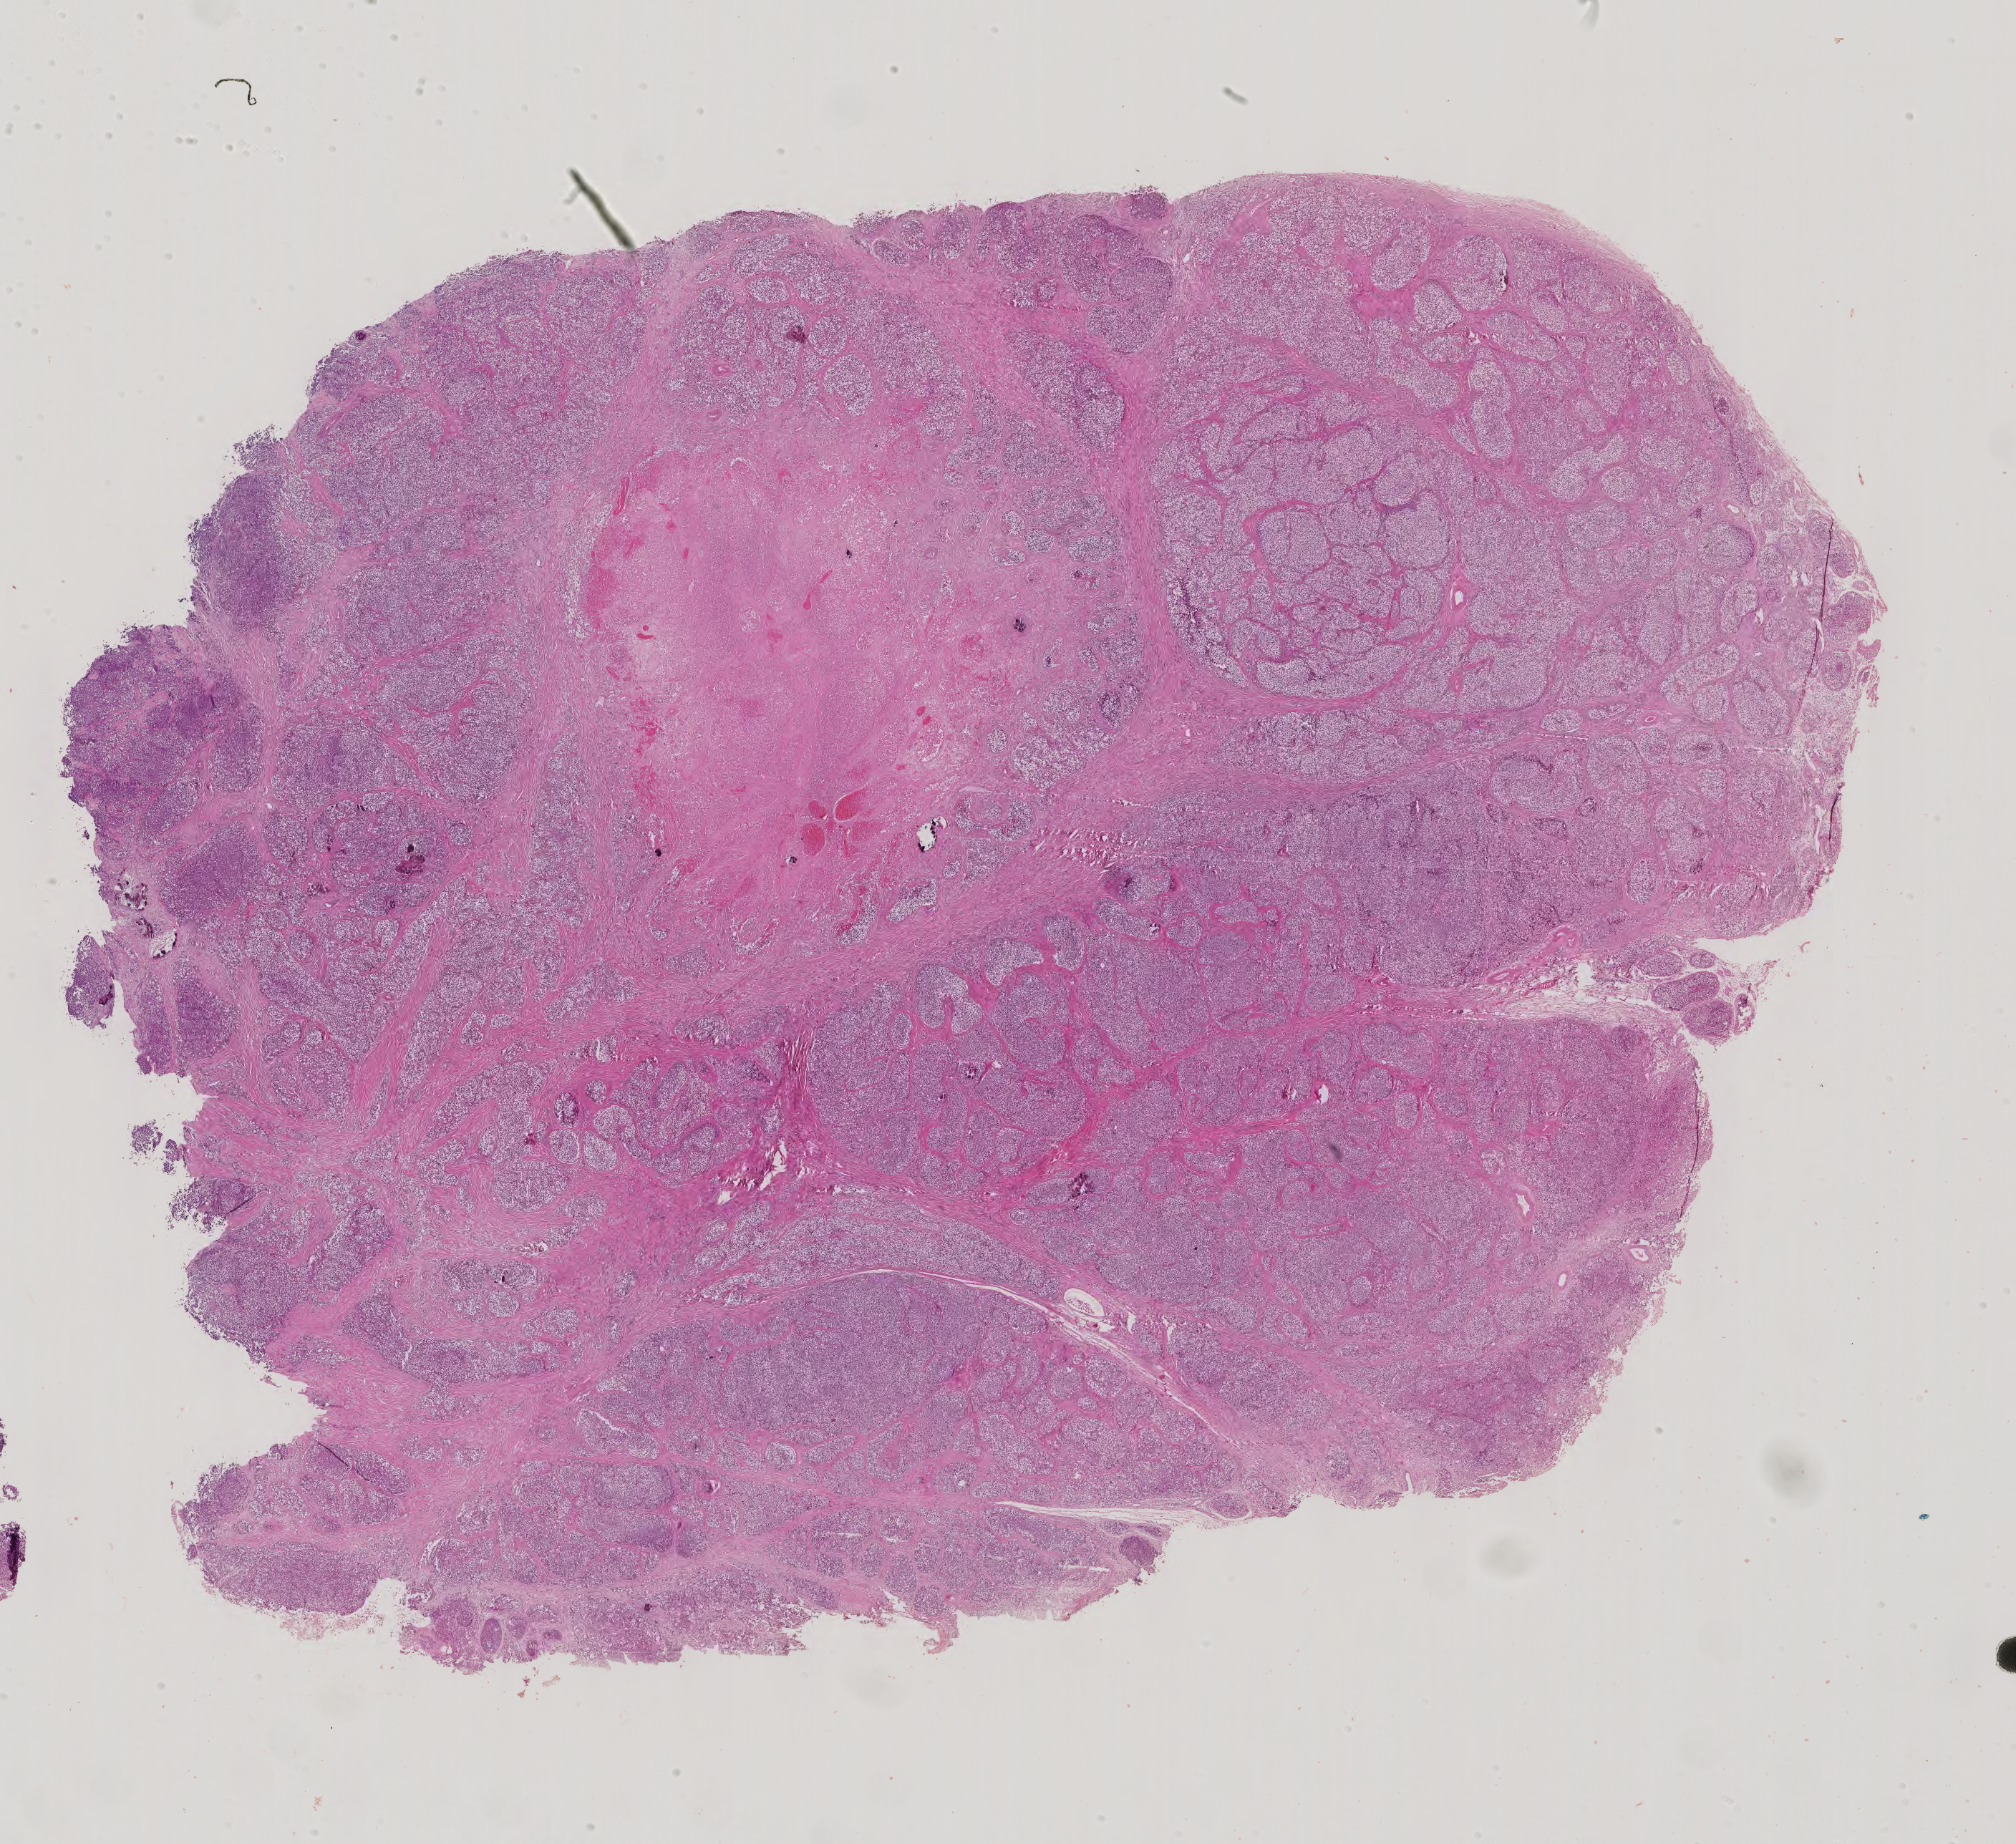
Whole-slide histology image, H&E-stained — a low-resolution overview of the entire scanned area, about 20.5 x 18.8 mm, formalin-fixed paraffin-embedded (FFPE) diagnostic section, primary tumour sample from the testis. Patient: male, age at initial diagnosis 20 years.
• AJCC pathologic stage: I (4th edition)
• diagnosis: Seminoma, NOS
• TNM: T2 NX M0
• laterality: right